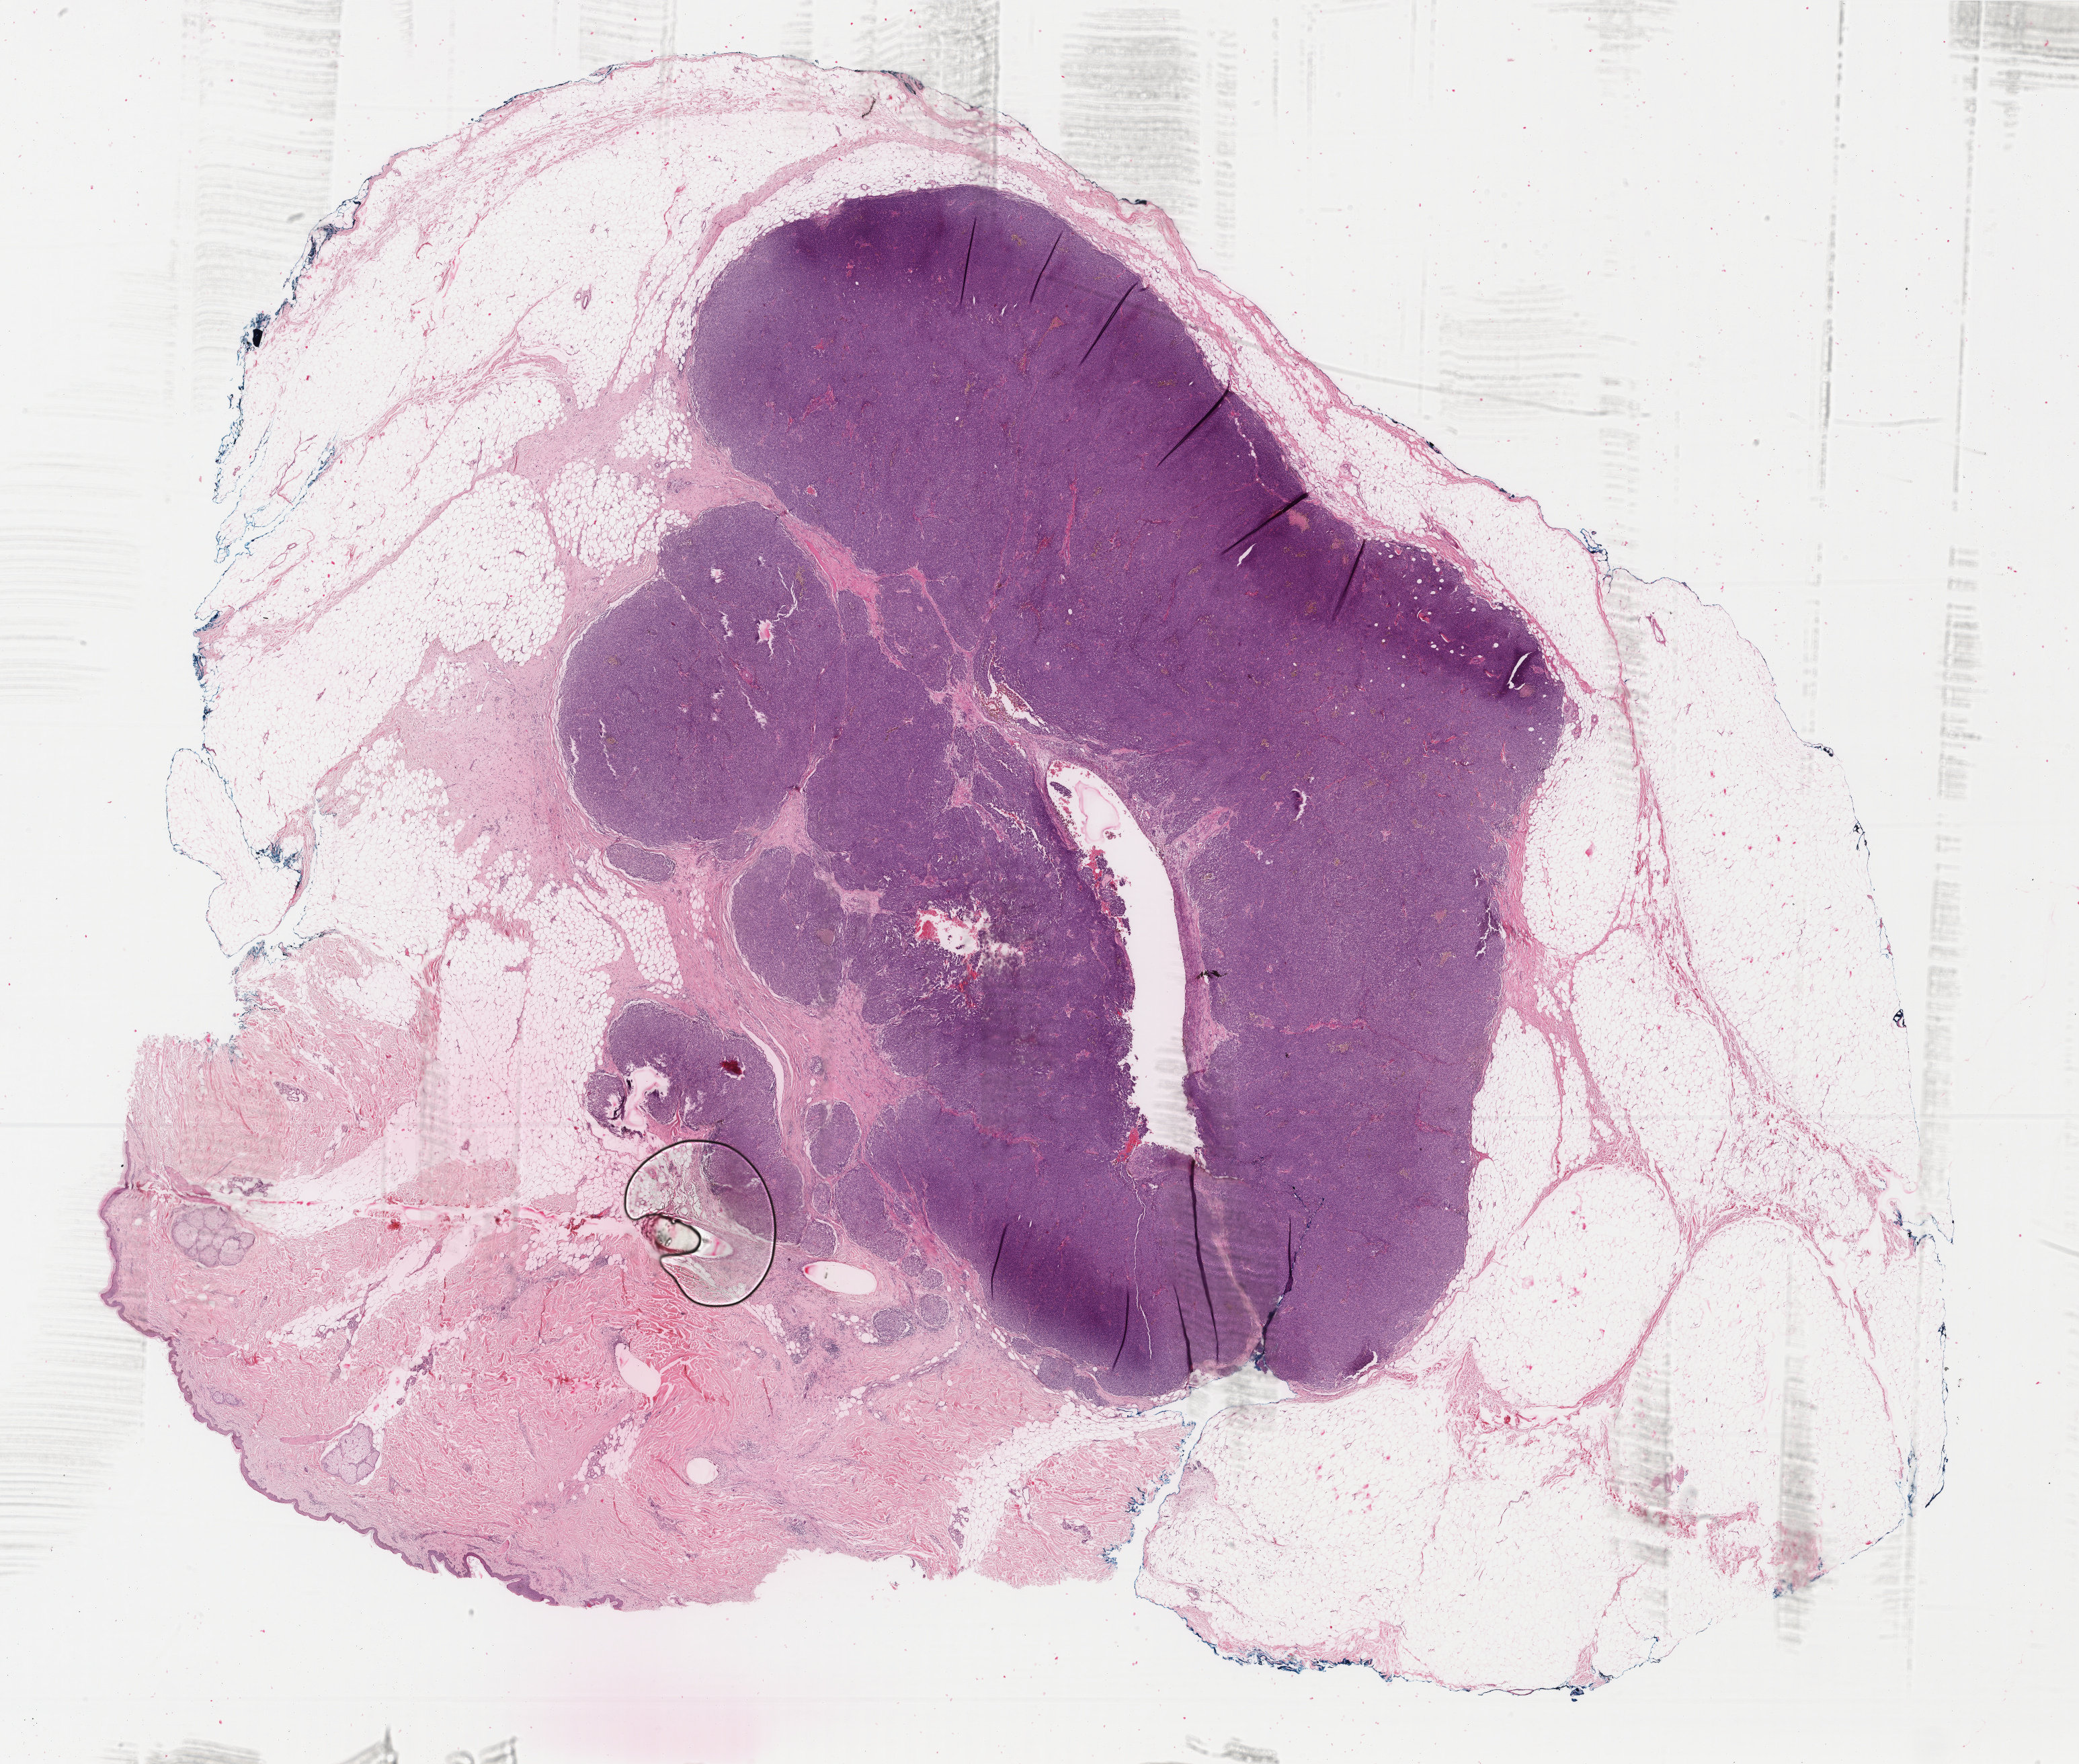
Hematoxylin and eosin (H&E) stained whole-slide image, shown as a low-resolution overview of the whole scanned area (about 24.6 x 20.8 mm, slide scanned at 40x), formalin-fixed paraffin-embedded (FFPE) diagnostic section, skin, primary tumour sample. Male, age 69 years at initial diagnosis.
- pathologic diagnosis: Malignant melanoma, NOS